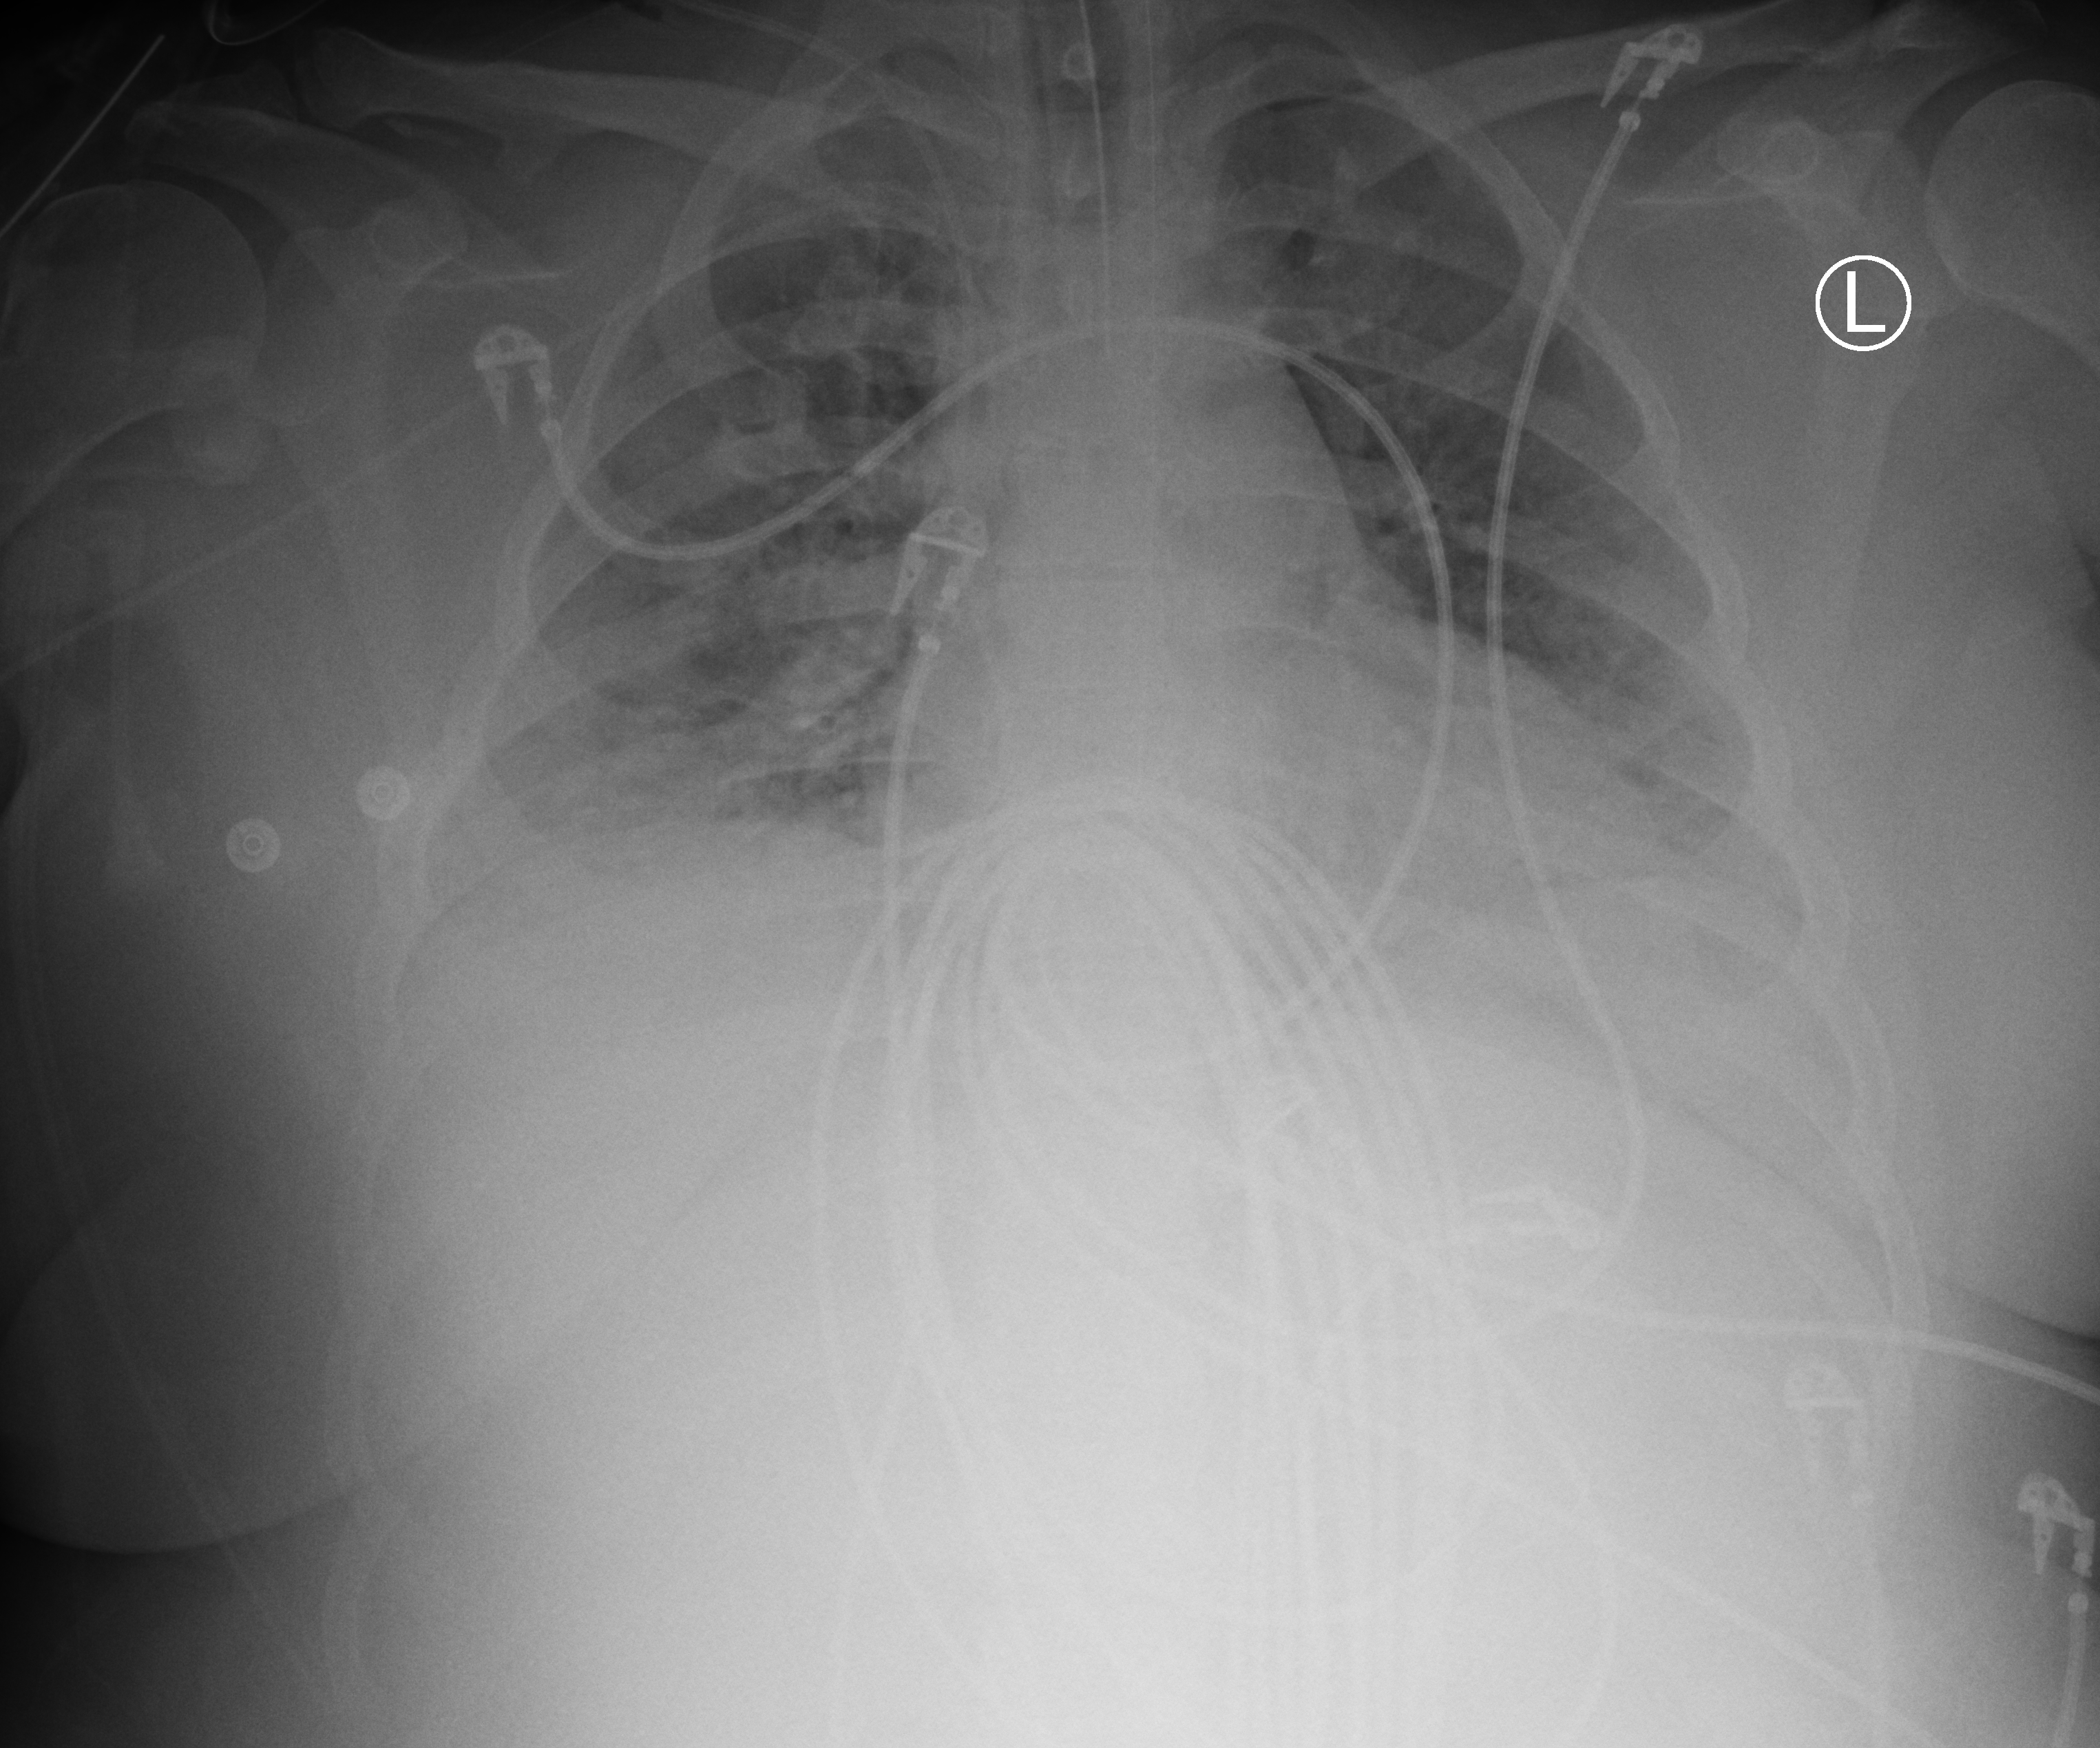
Portable chest radiograph, anteroposterior (AP) projection. Patient hospitalised with COVID-19; female, aged 18–59 years.
From the hospital-stay record, not from the radiograph (when in the stay this image was taken is not recorded):
- mechanically ventilated during this hospital stay: yes
- chronic kidney disease (admission record): no